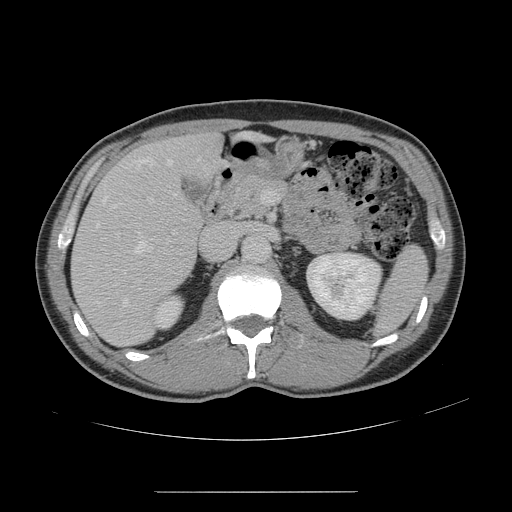
Contrast-enhanced abdominal CT, one axial slice; position 79 of 178 along the scan axis; 120 kVp; soft-tissue window (W 400 / L 40 HU); 2.5 mm slice thickness; 512 × 512 image matrix, field of view 401 × 401 mm. Male patient, age 53 years. From the clinical record (not read from this slice): diagnosis: colorectal cancer liver metastases, imaged before liver resection; multiple liver metastases: yes; largest metastasis: 2.4 cm; disease in both lobes: no.
Outlined on this slice (expert manual segmentation):
- hepatic veins: bounding box <96,157,172,307> (left, top, right, bottom; pixels)
- liver: <72,134,221,346>
- planned liver remnant (the part of the liver to remain after resection): <163,134,221,175>
- portal vein (with intrahepatic branches): <148,190,267,268>